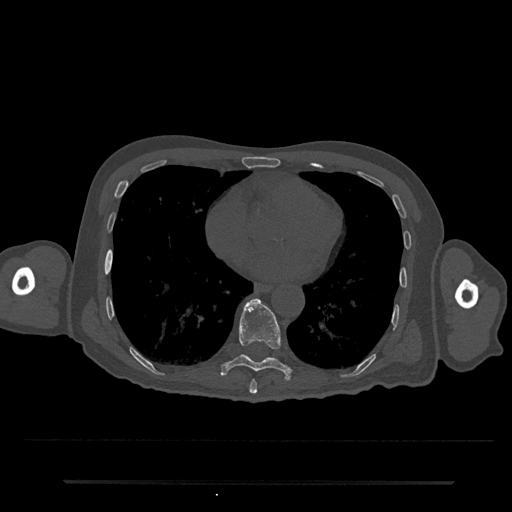
CT including the spine, one axial slice; slice 367 of 797 in the series (ordered by position); 120 kVp; bone window (W 1800 / L 400 HU); 0.5 mm slice thickness; 512 × 512 image matrix, field of view 427 × 427 mm. Male patient, age 74 years. From the clinical record (not read from this slice): primary cancer: prostate.
Structures marked on this image (semi-automatic segmentation, software-assisted and operator-edited):
- T8 vertebra: bounding box [x1, y1, x2, y2] px = [249, 380, 257, 394]
- T9 vertebra: [221, 298, 292, 380]